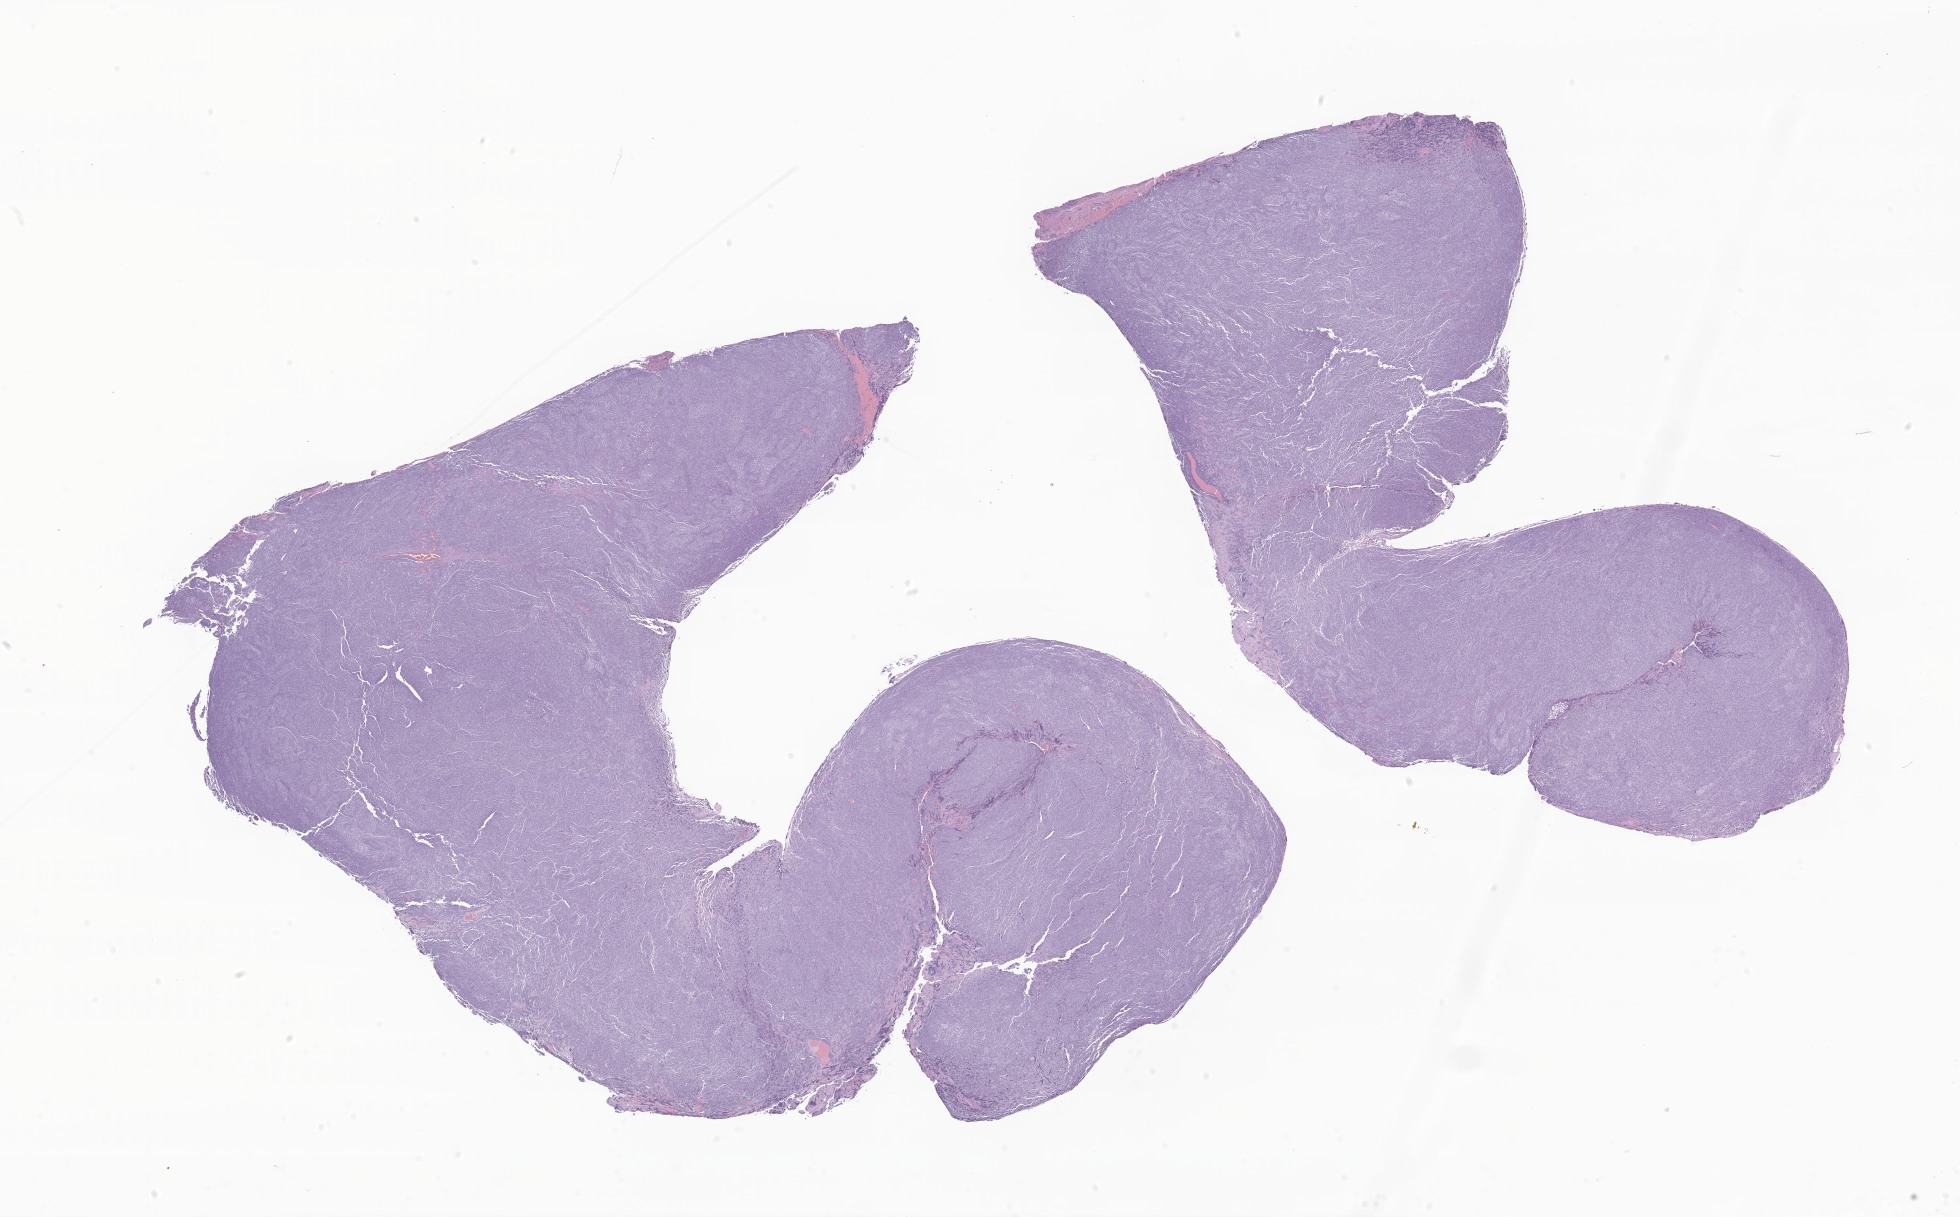
Whole-slide image, haematoxylin and eosin stain of tumor tissue from the brain, low-resolution overview of the scanned area, about 33.1 x 20.5 mm. Formalin-fixed paraffin-embedded section. Female patient, age 216 months (18 years).
- diagnosis (ICD-O-3 morphology term): Medulloblastoma, NOS